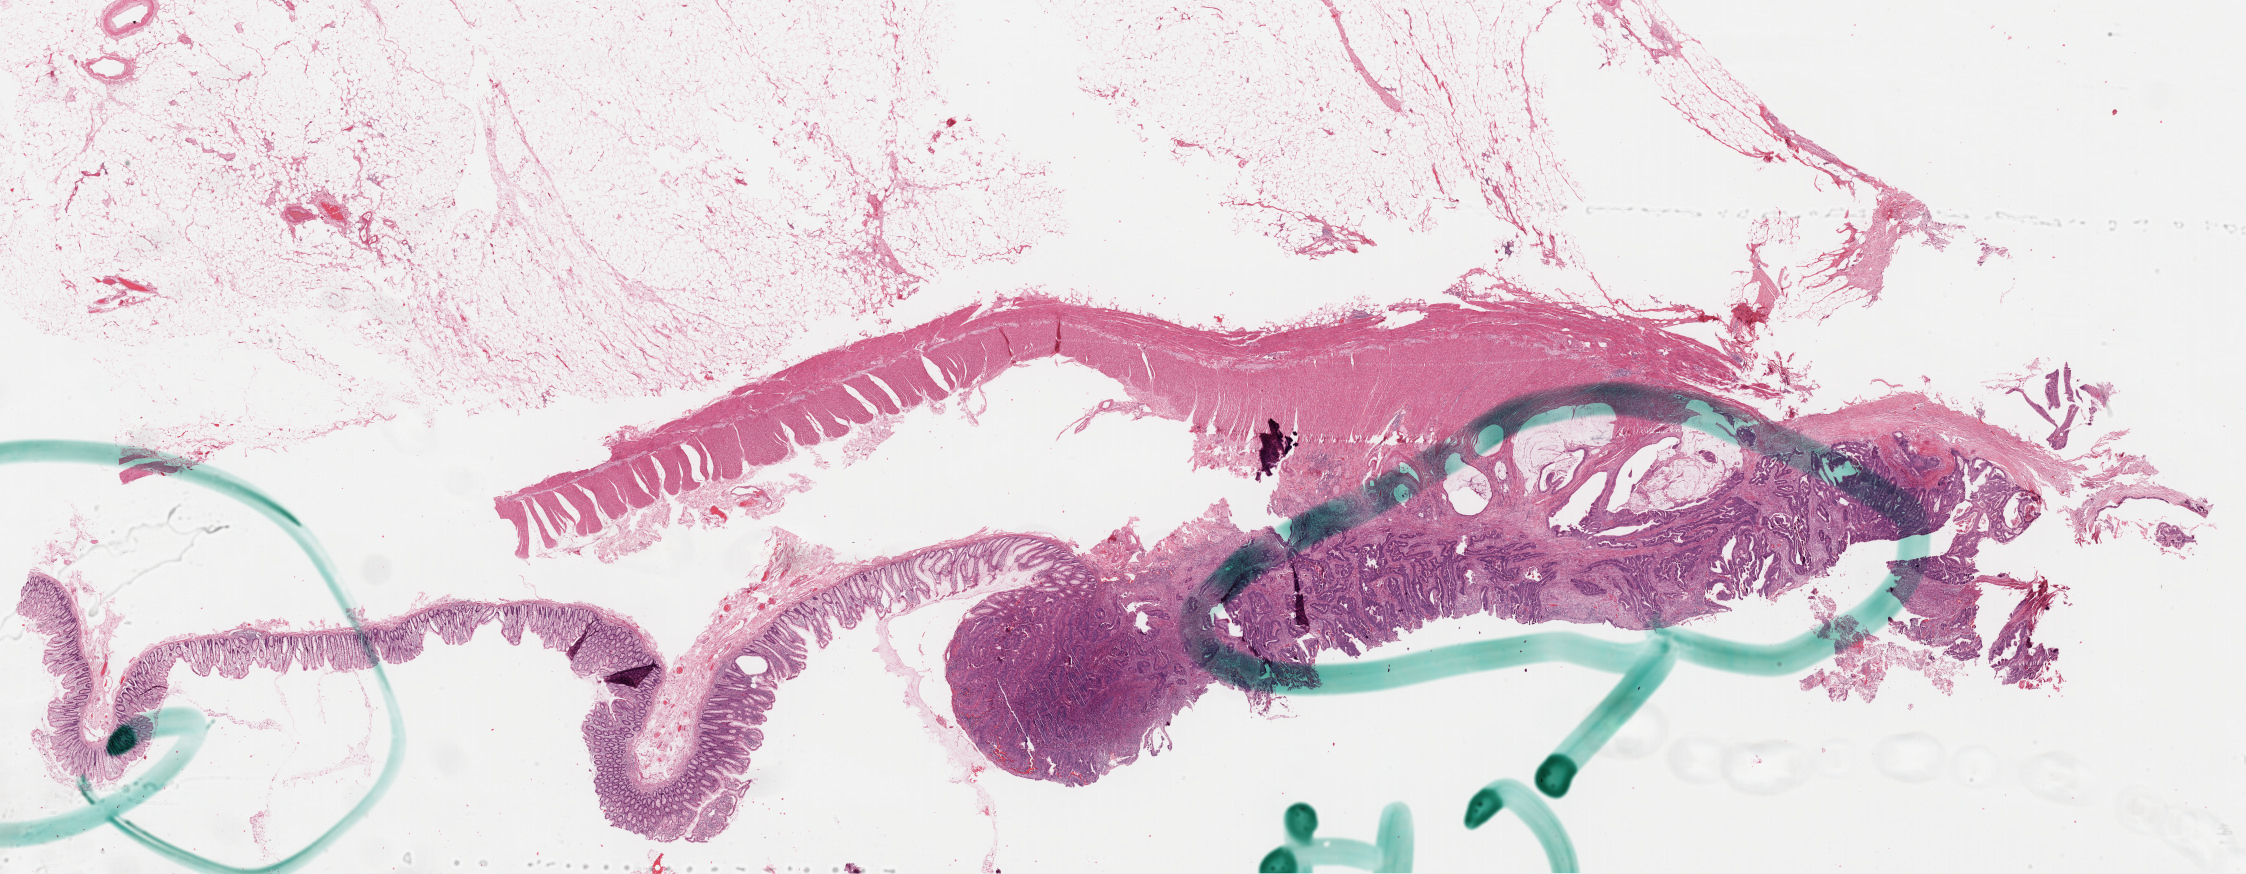
H&E whole-slide image, shown as a low-resolution overview of the whole scanned area (about 35.5 x 13.8 mm, slide scanned at 40x); formalin-fixed paraffin-embedded (FFPE) diagnostic section; sample: primary tumour, colon. Male patient; age at initial diagnosis 82 years.
Lymph nodes positive (case pathology): 0 of 15 examined. Pathologic diagnosis: Mucinous adenocarcinoma (sigmoid colon). TNM: T3 N0 M0. AJCC pathologic stage: IIA.